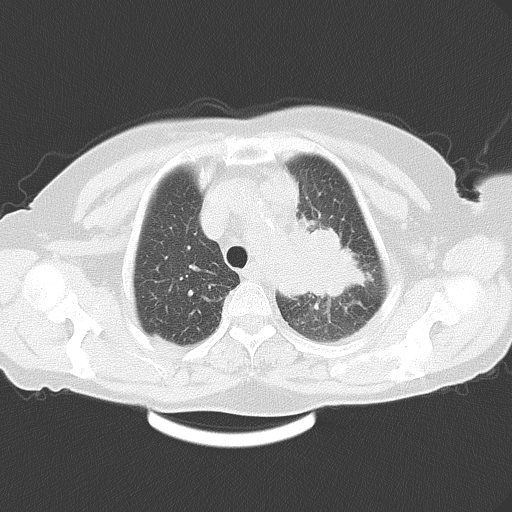
Chest CT, one axial slice; slice 43 of 54 in the series (ordered by position); reconstruction kernel B70f; 120 kVp; lung window (W 1500 / L -600 HU); 5 mm slice thickness; 512 × 512 image matrix. Patient: female, 71 years. From the clinical record (not read from this slice): clinical TNM (as recorded): T3 N3 M0.
Structures marked on this image (rectangle marked by the reading radiologist):
- lung tumour (recorded histology: adenocarcinoma): bounding box [x1, y1, x2, y2] px = [288, 216, 375, 314]